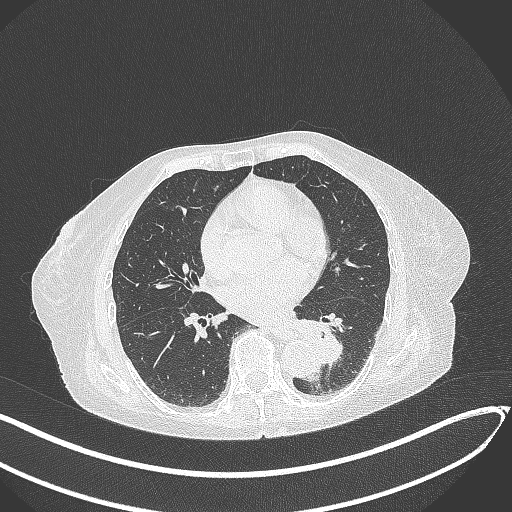
Chest CT, one axial slice; position 111 of 324 along the scan axis; lung window (W 1500 / L -600 HU); 1 mm slice thickness; 512 × 512 image matrix, field of view 400 × 400 mm. Female patient, age 82 years. From the clinical record (not read from this slice): clinical TNM (as recorded): T1b N0 M1.
Structures marked on this image (rectangle marked by the reading radiologist):
- lung tumour (recorded histology: adenocarcinoma): bounding box <296,315,350,366> (left, top, right, bottom; pixels)